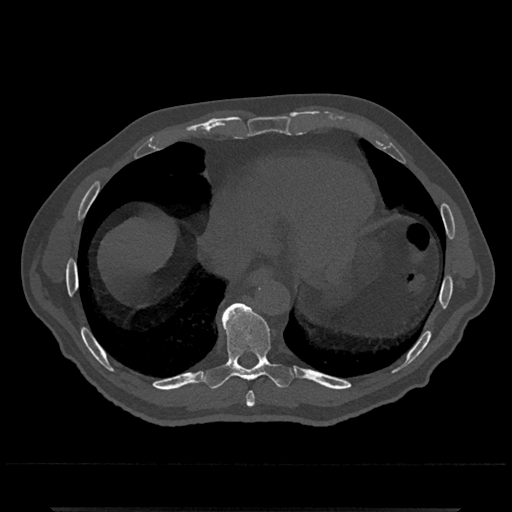
CT including the spine, one axial slice. Slice 618 of 797 in the series (ordered by position). Reconstruction kernel Br40s/3. Bone window (W 1800 / L 400 HU). 512 × 512 image matrix. Male patient, age 67 years. From the clinical record (not read from this slice): primary cancer: prostate.
Annotated regions visible in this slice (semi-automatic segmentation, software-assisted and operator-edited):
- T8 vertebra: bounding box [x1, y1, x2, y2] px = [246, 392, 255, 407]
- T9 vertebra: [204, 303, 295, 389]